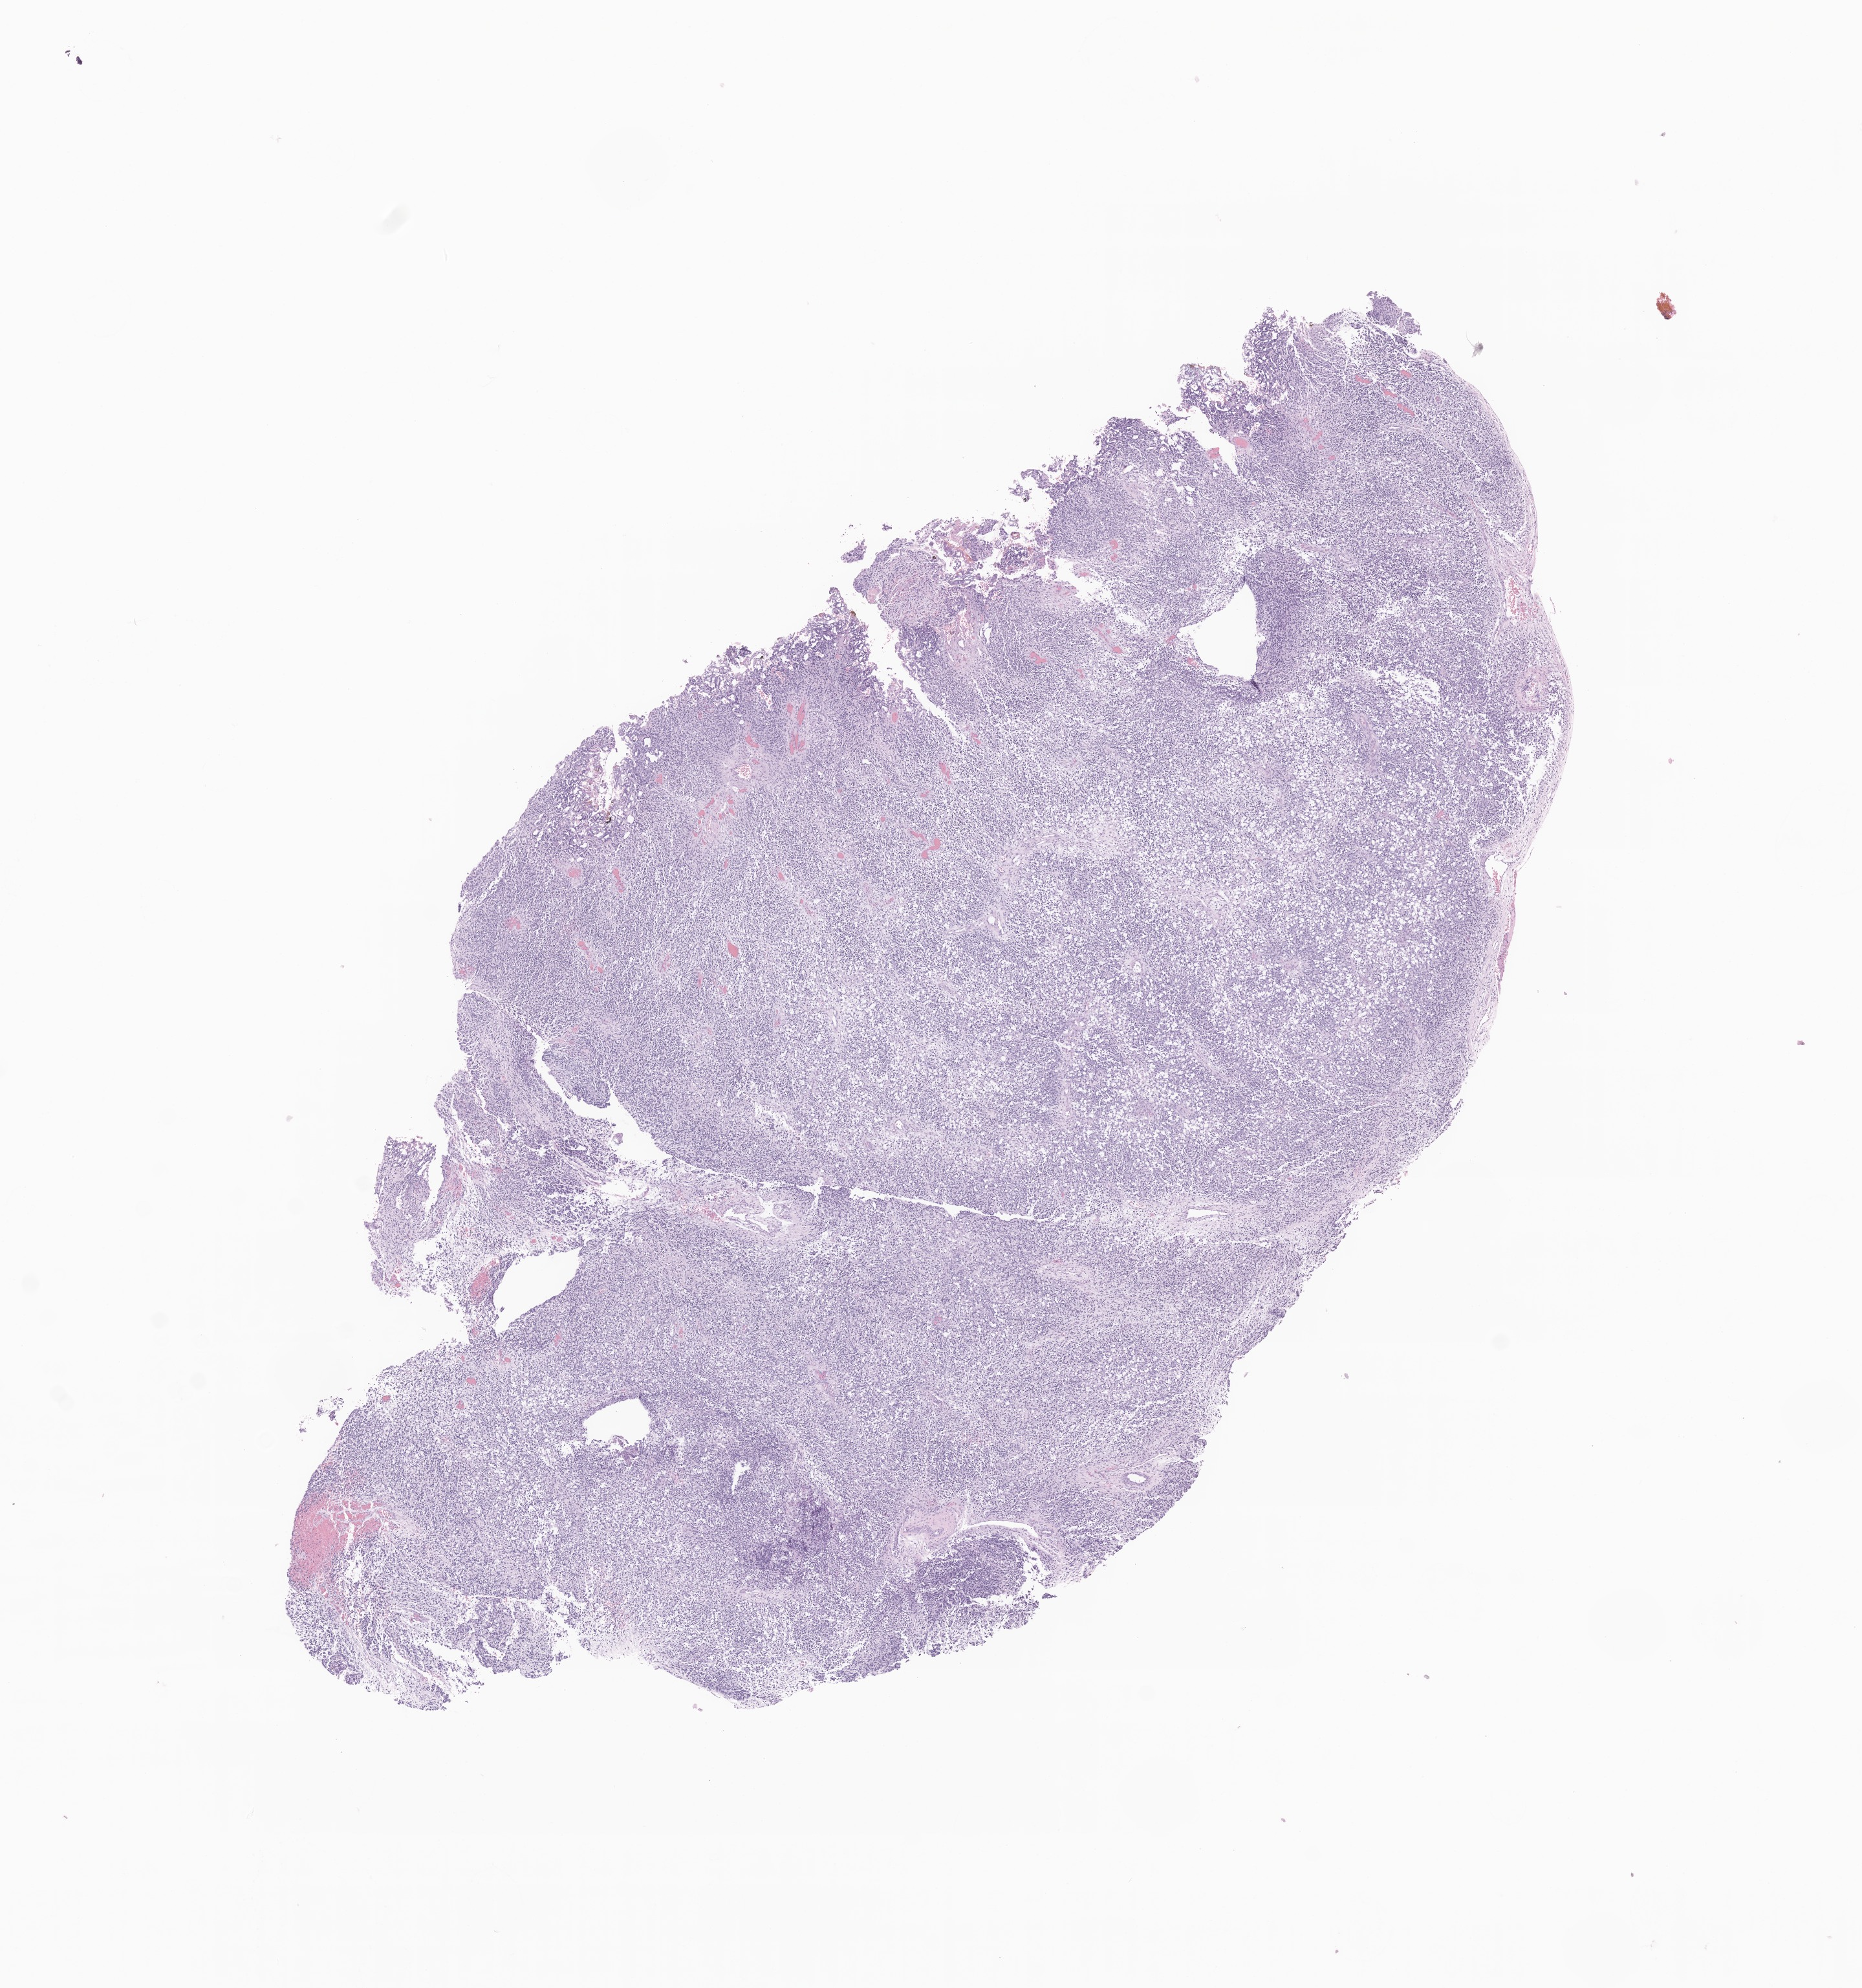
Haematoxylin and eosin whole-slide image of tumor tissue from the anus — shown as a low-resolution overview of the whole scanned area (about 12.1 x 13.0 mm), FFPE section. Male patient, age 115 months (9 years 7 months).
Recorded diagnosis: Rhabdomyosarcoma, NOS.